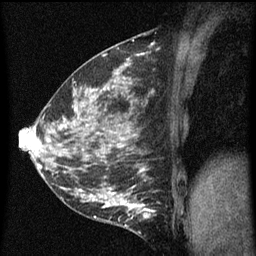
Breast MRI (dynamic contrast-enhanced), one sagittal slice; position 24 of 60 along the scan axis; dynamic contrast-enhanced series, image 2 of 5 at this slice position (ordered by acquisition); 1.5 T; TE 4.2 ms, TR 8 ms; 2 mm slice thickness; 256 × 256 image matrix, field of view 180 × 180 mm. Female patient, age 35 years.
Structures marked on this image (semi-automatically segmented with operator editing):
- analysis volume of interest (the breast-tissue region the enhancement analysis was run in; not a lesion): box from (x=118, y=190) to (x=157, y=229) px
- tumour enhancement mask (voxels above the 70 % enhancement threshold inside the analysis volume of interest): (x=118, y=198)–(x=155, y=227)